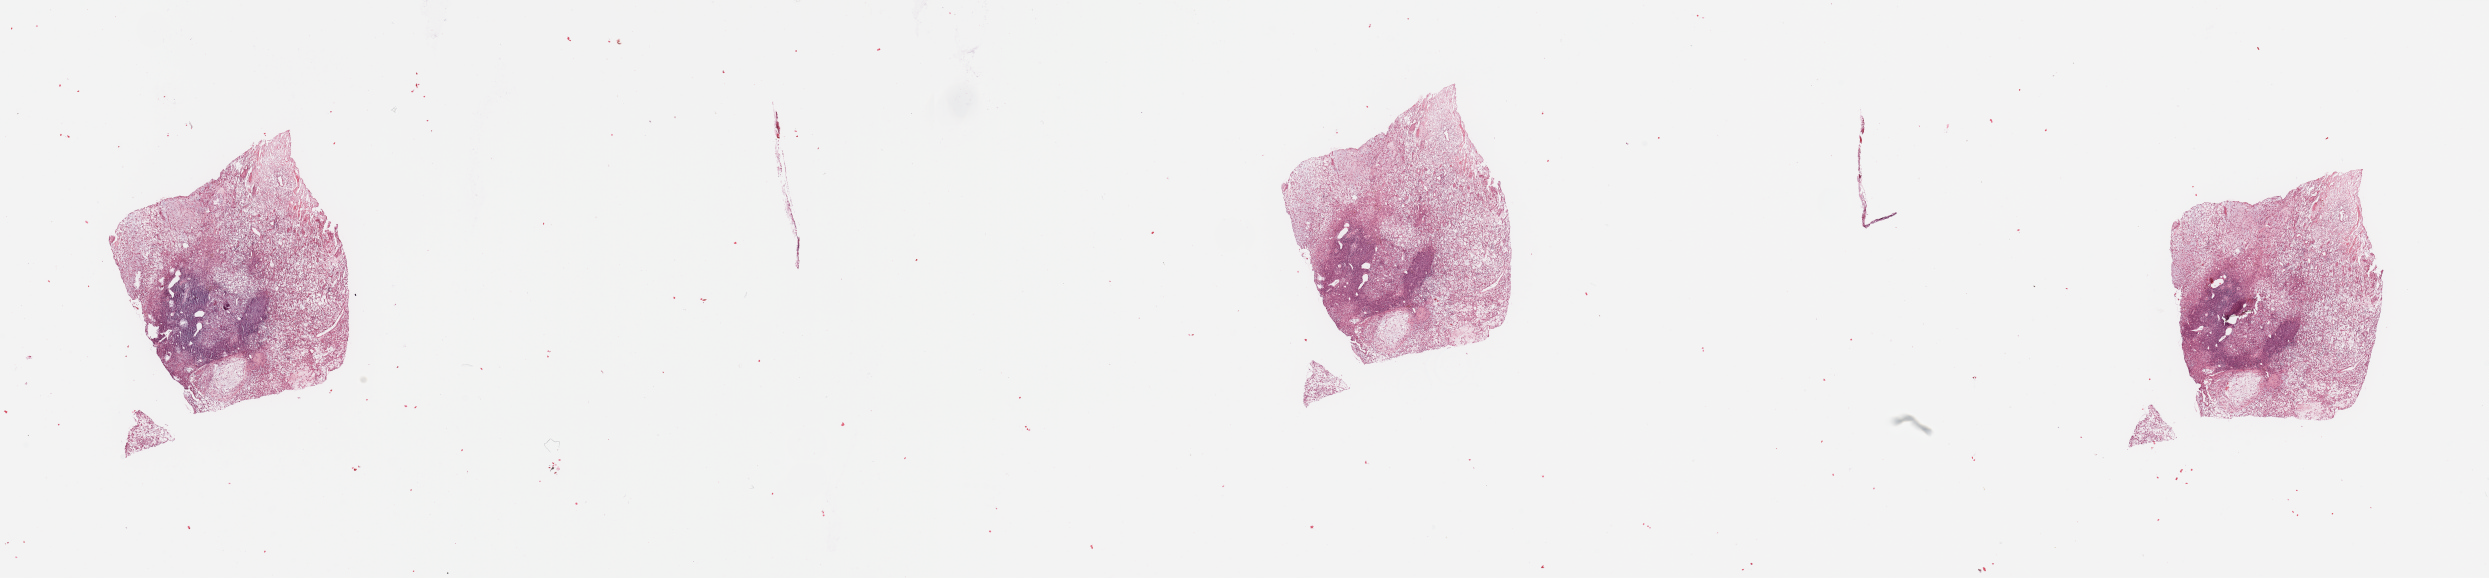
Digitized H&E-stained tissue section (whole slide), shown as a low-resolution overview of the whole scanned area (about 39.4 x 9.1 mm), kidney, tumour tissue. 68-year-old male patient. Histologic grade: G1 (well differentiated).
* diagnosis: Renal cell carcinoma, NOS
* primary tumour site (as recorded): middle
* AJCC pathologic stage: I